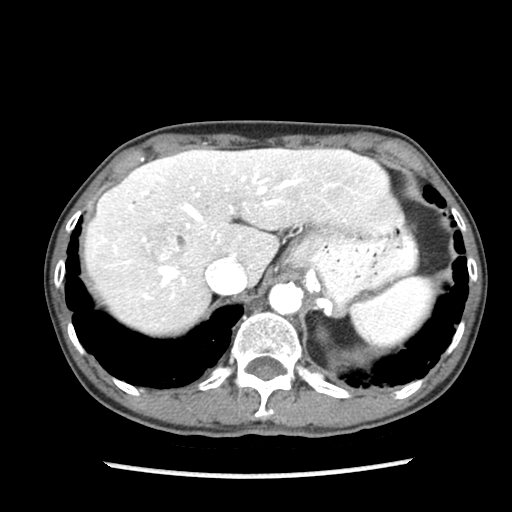
Contrast-enhanced abdominal CT (liver protocol), one axial slice; slice 64 of 87 in the series (ordered by position); reconstruction kernel STANDARD; soft-tissue window (W 400 / L 40 HU); 512 × 512 image matrix, field of view 300 × 300 mm. Case-level facts recorded for this patient, not image findings: diagnosis: hepatocellular carcinoma (patient treated with transarterial chemoembolisation; whether this scan precedes or follows treatment is not stated here); TNM stage (as recorded): Stage-IIIB; Child-Pugh class: A.
Annotated regions visible in this slice (semi-automatic segmentation, software-assisted and operator-edited):
- liver parenchyma outside the tumour (the mass and vessels are separate outlines, so this box may not span the whole liver): bounding box <84,148,394,334> (left, top, right, bottom; pixels)
- mass: <146,228,185,262>
- liver vessels: <114,159,298,299>